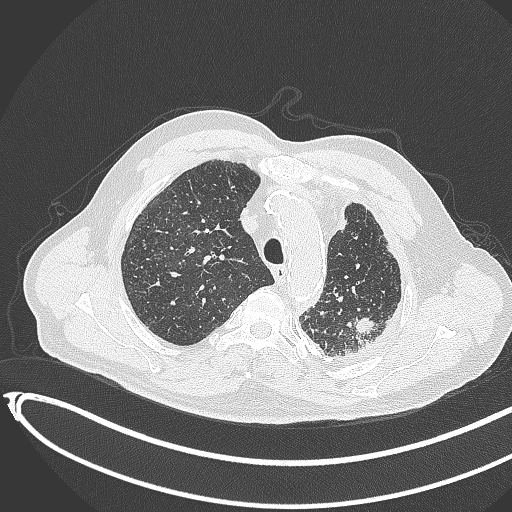
Chest CT, one axial slice. Reconstruction kernel B70f. 120 kVp. Lung window (W 1500 / L -600 HU). 1 mm slice thickness. 512 × 512 image matrix, field of view 400 × 400 mm. Patient: male, 78 years. From the clinical record (not read from this slice): clinical TNM (as recorded): T1c N0 M1.
Annotated regions visible in this slice (rectangle marked by the reading radiologist):
- lung tumour (recorded histology: adenocarcinoma): bounding box <348,312,383,346> (left, top, right, bottom; pixels)